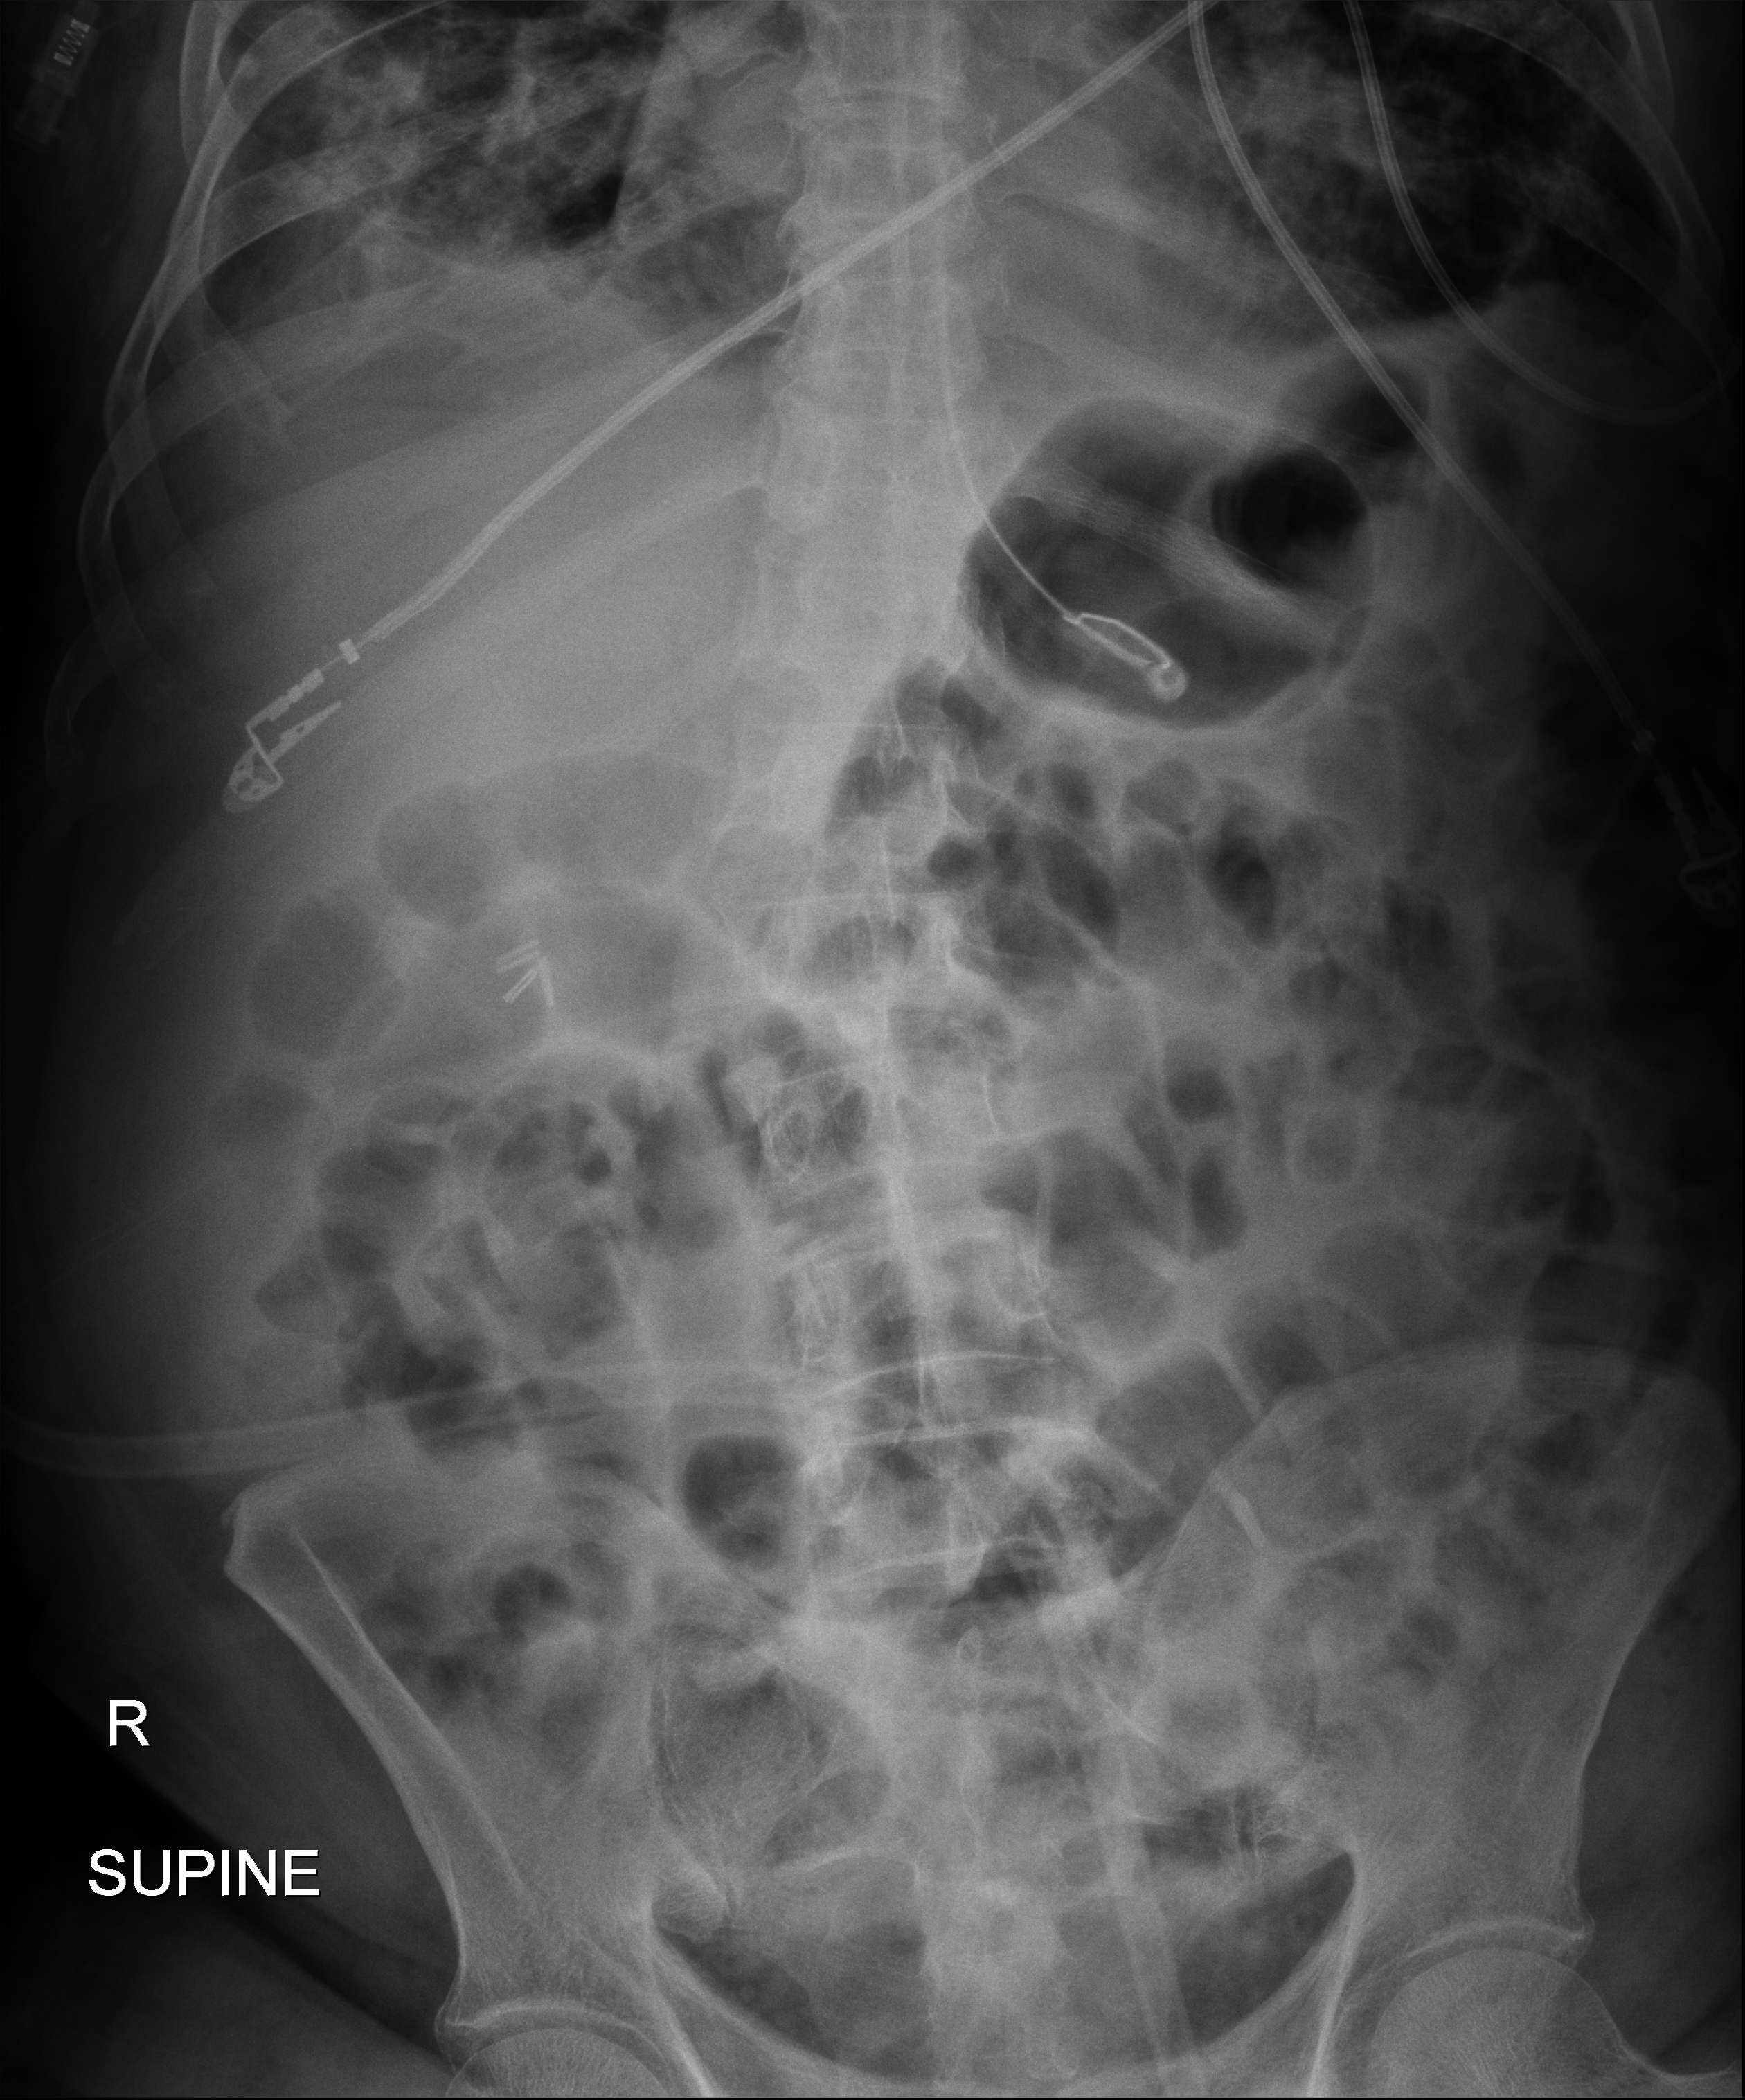
Portable abdomen radiograph. Patient hospitalised with COVID-19; male, aged 75–90 years.
Hospital-stay facts (about this admission, not read from this image; timing relative to this image not recorded):
- mechanically ventilated during this hospital stay: yes
- admitted to intensive care during this hospital stay: yes